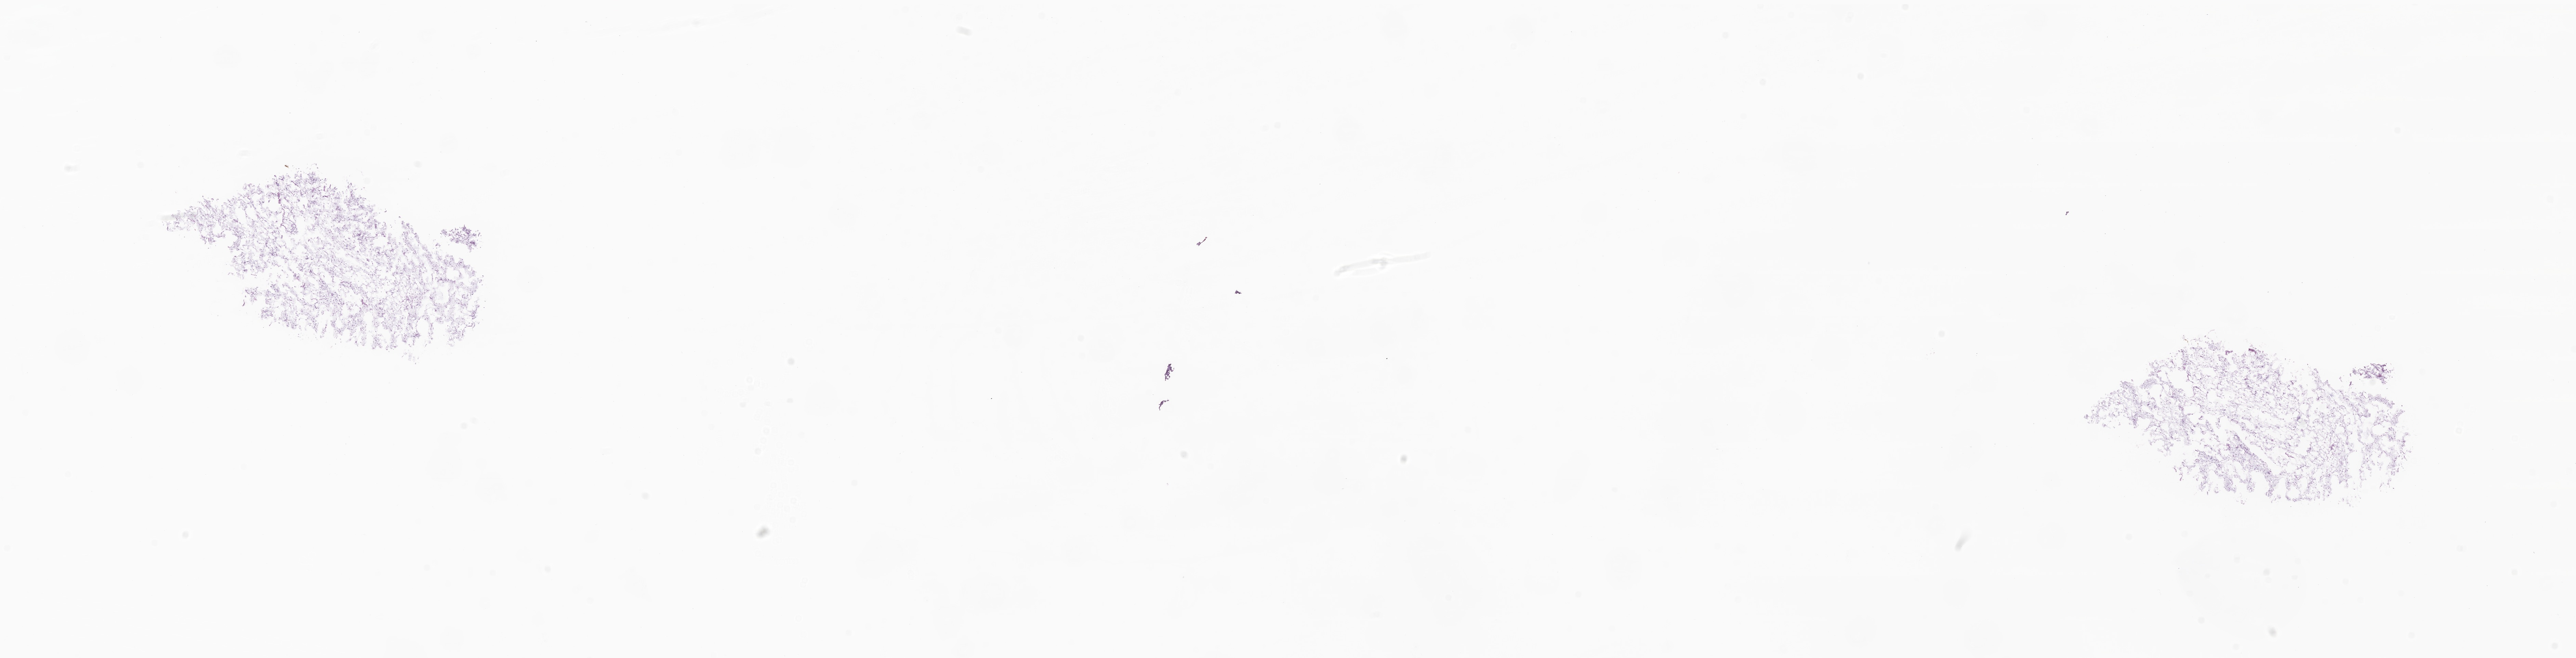
Haematoxylin and eosin whole-slide image of tumor tissue from the soft tissue of lower extremity, whole scanned area (about 31.8 x 8.1 mm) shown as a low-resolution overview, frozen section (OCT-embedded). Female patient, age 230 months.
Diagnosis (ICD-O-3 morphology term): Myxoid liposarcoma.